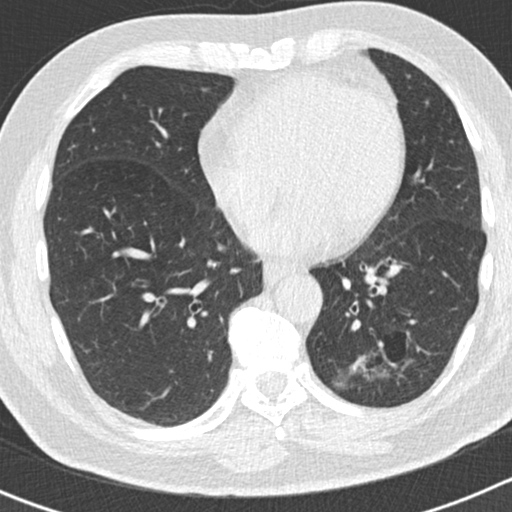
Chest CT (low-dose screening protocol), one axial image, second screening round (one year after baseline), lung window (W 1500 / L -600 HU), 2 mm slice thickness, standard (soft-tissue) reconstruction kernel (B30f), slice 102 of 186 in the series. Male, age 66 years at enrolment. Former smoker at enrolment.
- Expert-annotated lung lesion, bounding box [x1, y1, x2, y2] px = [345, 322, 417, 402].
- Reader record for this screening exam (exam-level; its link to the box is not recorded): non-calcified nodule or mass ≥4 mm, left lower lobe, 50 × 33 mm, smooth margins, pre-existing on the prior screen: yes; interval growth: yes.